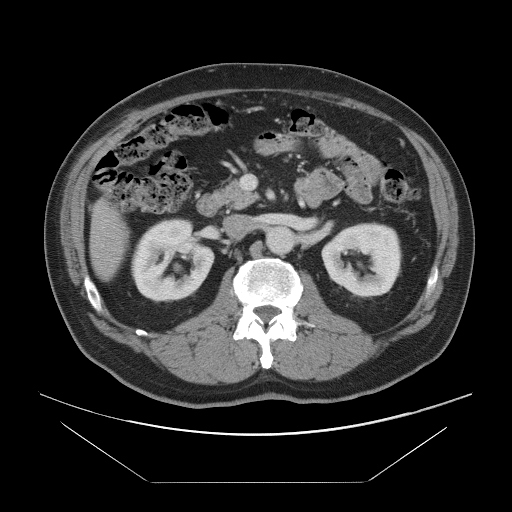
Contrast-enhanced abdominal CT, one axial slice; slice 38 of 97 in the series (ordered by position); intravenous contrast given; soft-tissue window (W 400 / L 40 HU); 5 mm slice thickness; 512 × 512 image matrix. Male patient, age 62 years. From the clinical record (not read from this slice): diagnosis: colorectal cancer liver metastases, imaged before liver resection; multiple liver metastases: no; largest metastasis: 7 cm; disease in both lobes: yes.
Annotated regions visible in this slice (manually delineated by an expert):
- liver: bounding box (x1, y1, x2, y2) in pixels: (91, 202, 126, 279)
- planned liver remnant (the part of the liver to remain after resection): (92, 203, 127, 279)